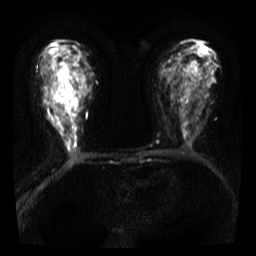
Breast MRI, one axial slice. Diffusion-weighted series; image 2 of 4 stored at this slice position (different b-values; order by instance number). 3 T. 5 mm slice thickness. 256 × 256 image matrix, field of view 300 × 300 mm. Female patient.
Outlined on this slice (expert manual segmentation):
- tumour on diffusion-weighted imaging: box from (x=51, y=56) to (x=68, y=104) px